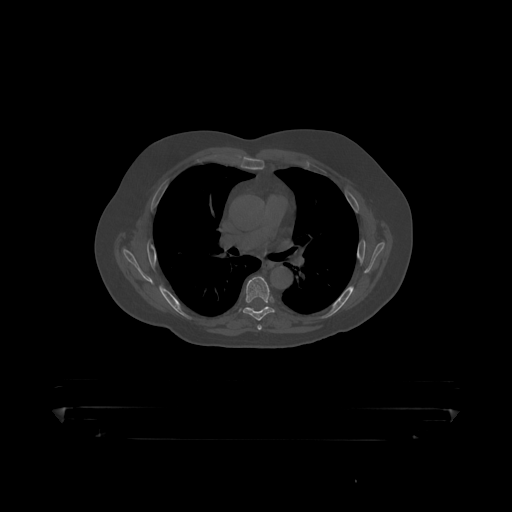
CT including the spine, one axial slice. Reconstruction kernel STANDARD. 120 kVp. Bone window (W 1800 / L 400 HU). 1.25 mm slice thickness. 512 × 512 image matrix, field of view 650 × 650 mm. Patient: male, 60 years. Case-level facts recorded for this patient, not image findings: primary cancer: prostate.
Structures marked on this image (semi-automatically segmented with operator editing):
- T6 vertebra: box from (x=243, y=277) to (x=275, y=319) px
- T7 vertebra: (x=246, y=308)–(x=250, y=309)